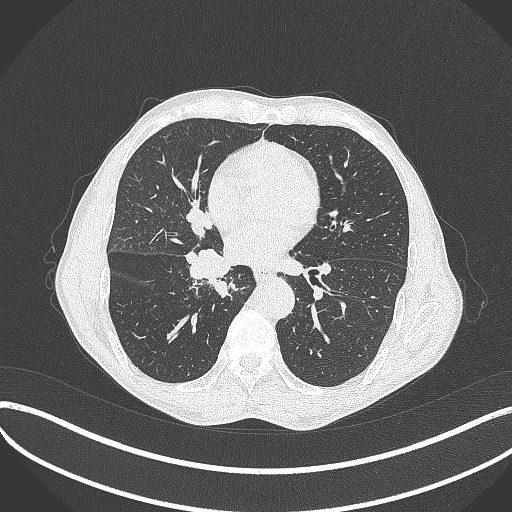
Chest CT, one axial slice; reconstruction kernel B70f; 120 kVp; lung window (W 1500 / L -600 HU); 1 mm slice thickness; 512 × 512 image matrix, field of view 400 × 400 mm. Male patient, age 65 years. Case-level facts recorded for this patient, not image findings: clinical TNM (as recorded): T2a N0 M0.
Structures marked on this image (bounding box drawn by a radiologist):
- lung tumour (recorded histology: squamous cell carcinoma): bounding box <177,240,234,302> (left, top, right, bottom; pixels)